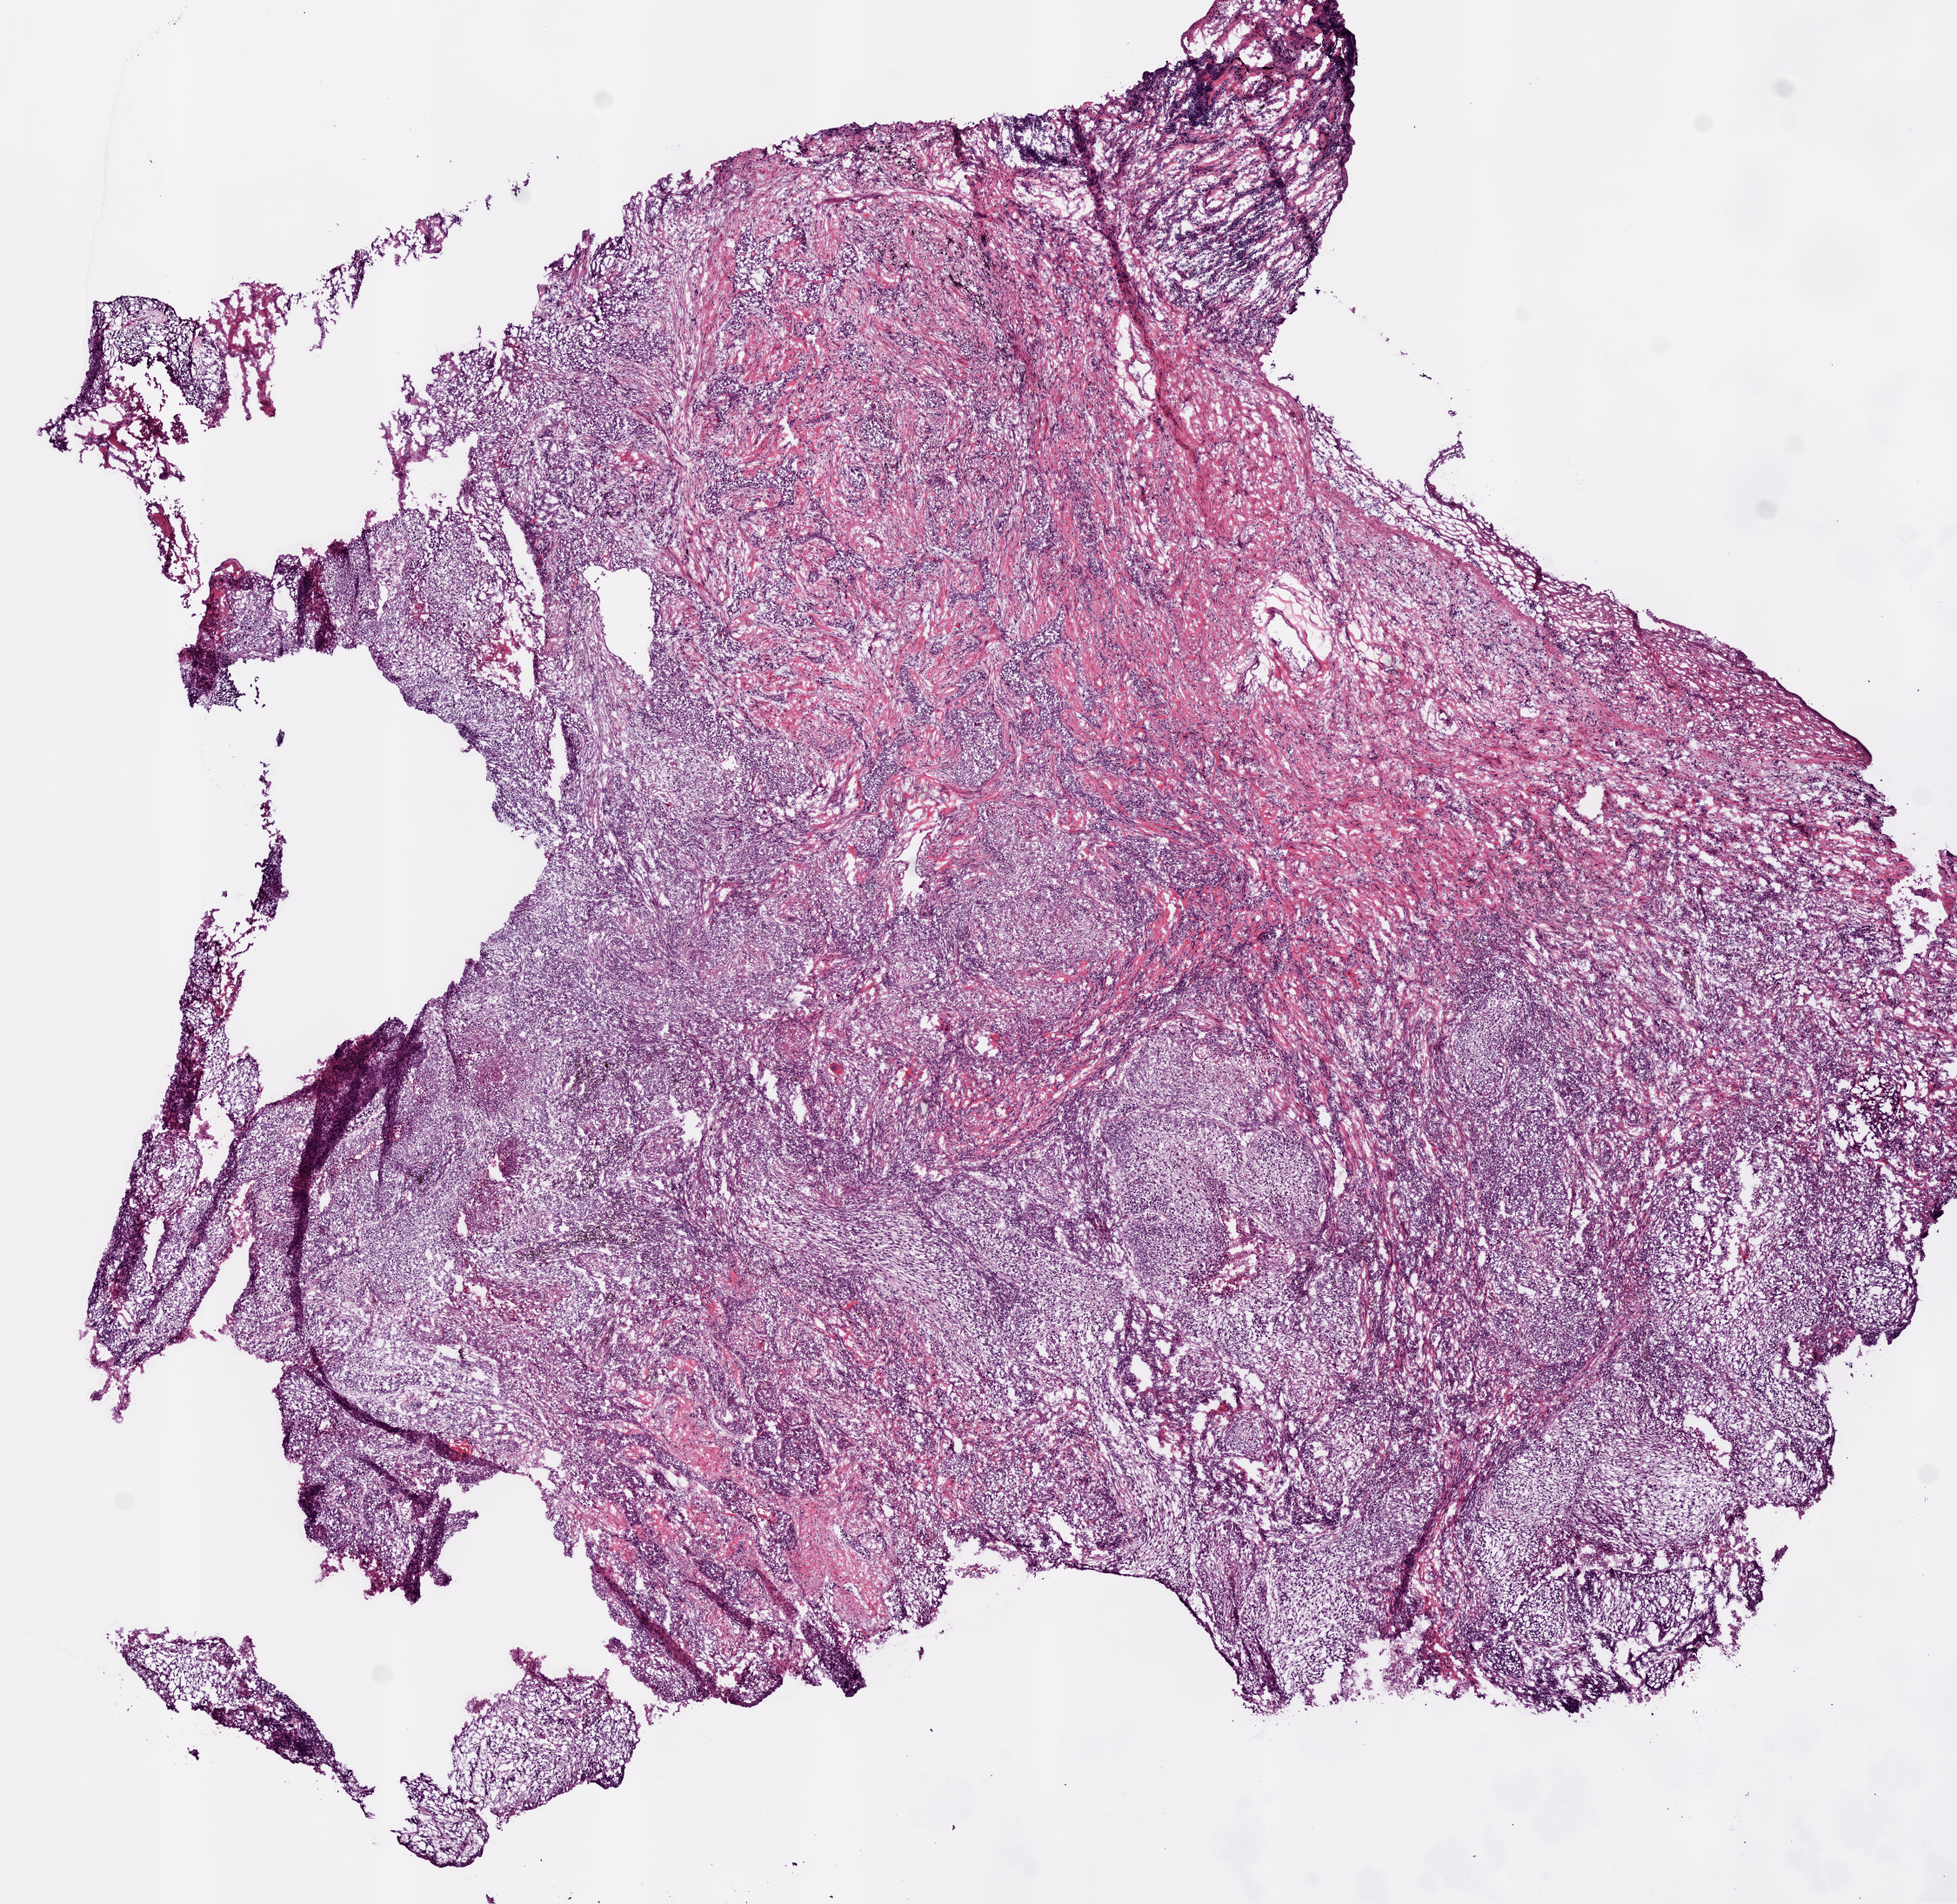
Digitized Hematoxylin and eosin (H&E) stained tissue section (whole slide) — low-resolution overview of the scanned area, about 9.0 x 8.8 mm (acquisition: 20x scan), frozen section from the bottom of the tissue portion, sample: primary tumour, lung. Male patient; age at initial diagnosis 64 years. Pathologist review of this section (percent, as recorded): tumour cells 85%, tumour nuclei 80%, normal cells 0%, stromal cells 10%, necrosis 5%. Inflammatory infiltration, as recorded: lymphocyte infiltration 5%, monocyte infiltration 5%, neutrophil infiltration 5%.
Histologic diagnosis: Squamous cell carcinoma, NOS (upper lobe, lung). AJCC pathologic stage: IB.